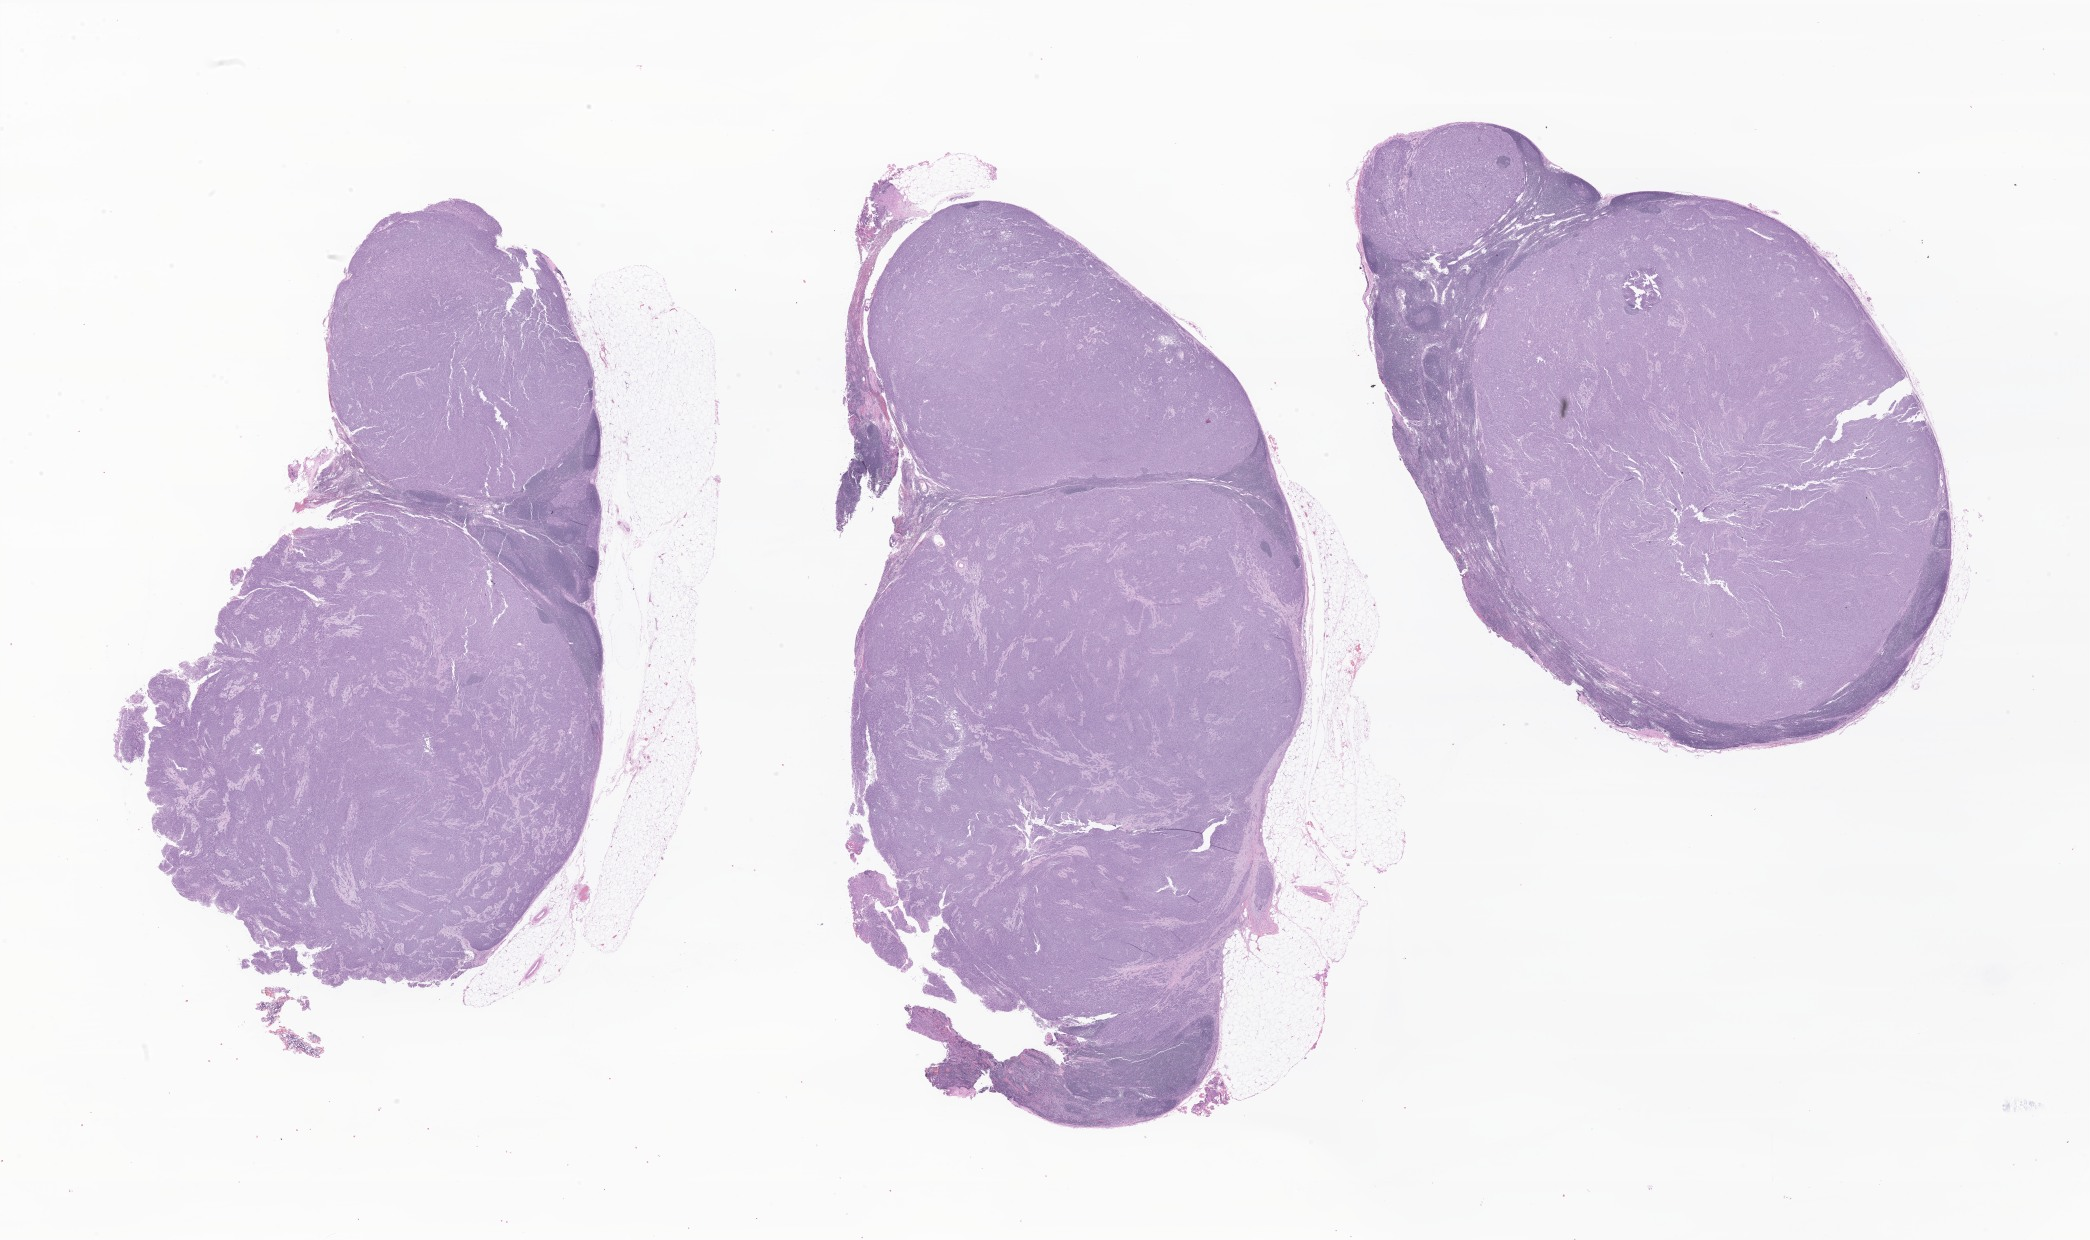
Digitized haematoxylin and eosin-stained section of tumor tissue from the soft tissue of lower extremity, whole scanned area (about 35.3 x 20.9 mm) shown as a low-resolution overview; FFPE section. Patient female; age 116 months.
• diagnosis (ICD-O-3 morphology term): Clear cell sarcoma, NOS